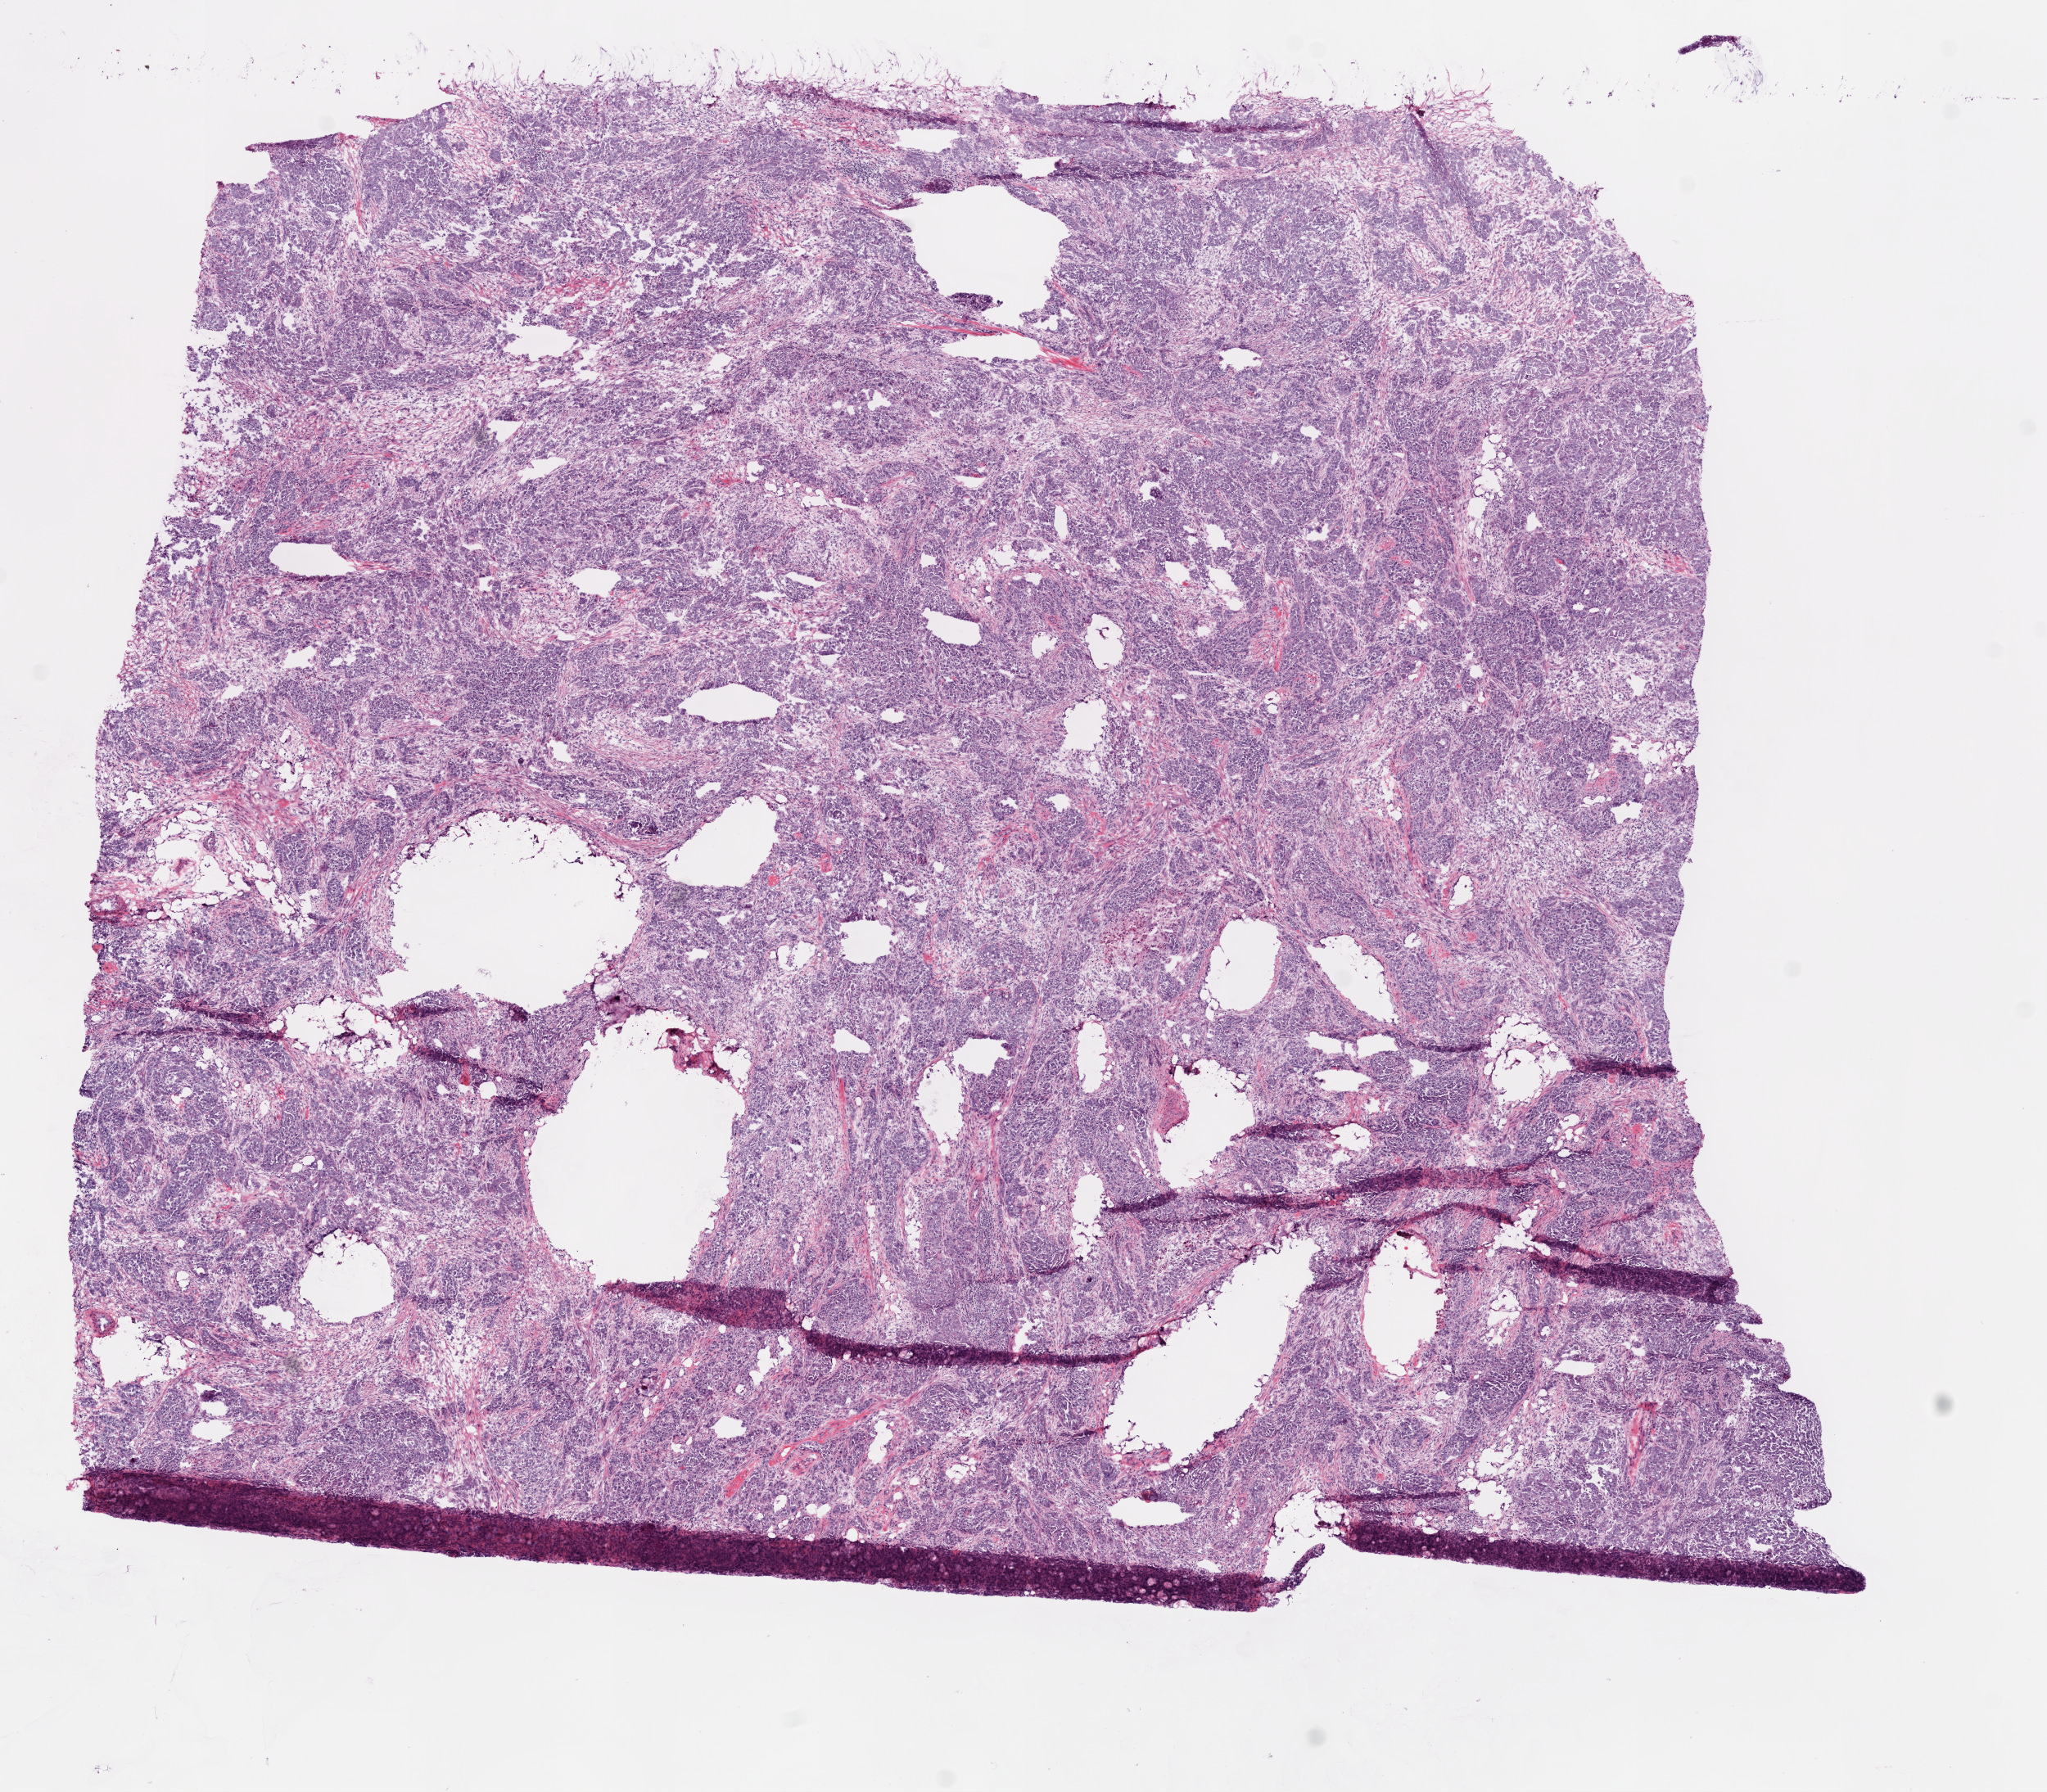
H&E-stained whole-slide image — a low-resolution overview of the entire scanned area, about 10.0 x 8.8 mm (slide scanned at 20x); frozen section from the bottom of the tissue portion; ovary, primary tumour sample. Patient: female, age at initial diagnosis 61 years. Histologic grade: G3 (poorly differentiated). Composition of this section per pathologist review: tumour cells 100%, tumour nuclei 60%, normal cells 0%, stromal cells 0%, necrosis 0%.
Laterality: bilateral. Diagnosis: Serous cystadenocarcinoma, NOS. FIGO stage: IV.